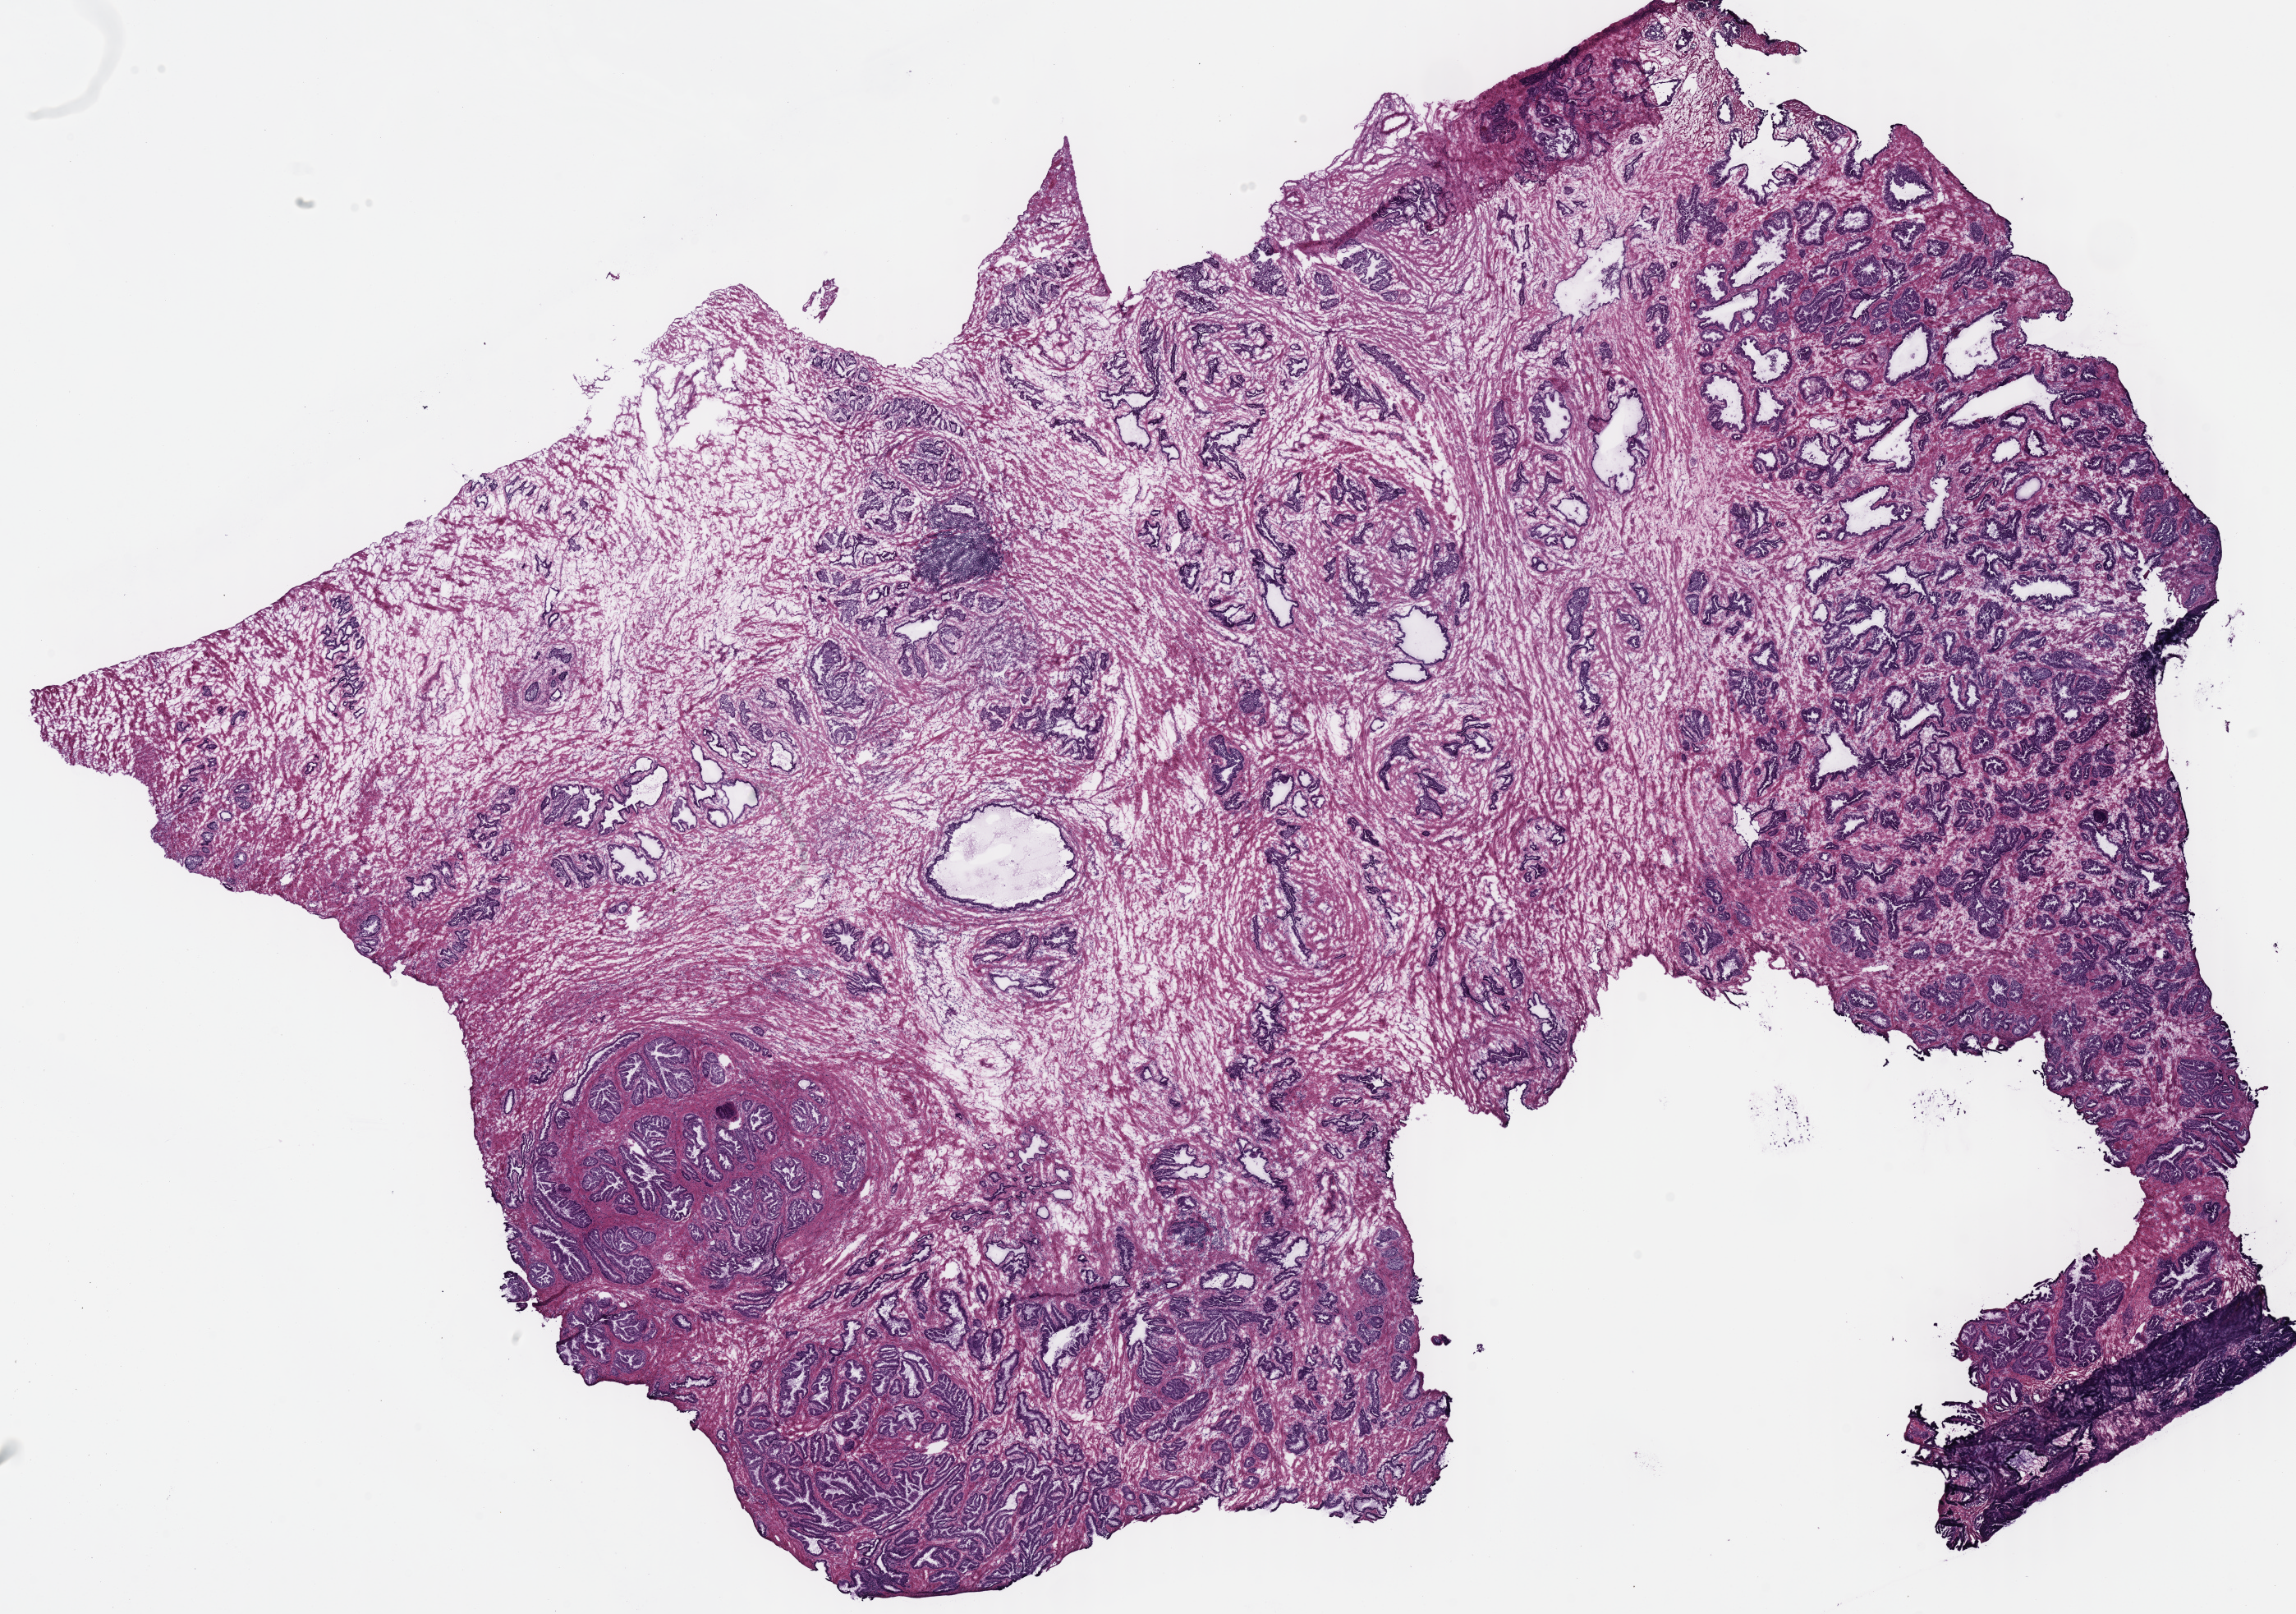
Hematoxylin and eosin (H&E) stained whole-slide image — low-resolution overview of the scanned area, about 22.0 x 15.5 mm; frozen section from the top of the tissue portion; sample: solid tissue normal (non-tumour tissue), prostate. Male, age 57 years at initial diagnosis.
This section: solid tissue normal (non-tumour) sample from the same patient. Patient diagnosis: Acinar cell carcinoma (prostate gland).